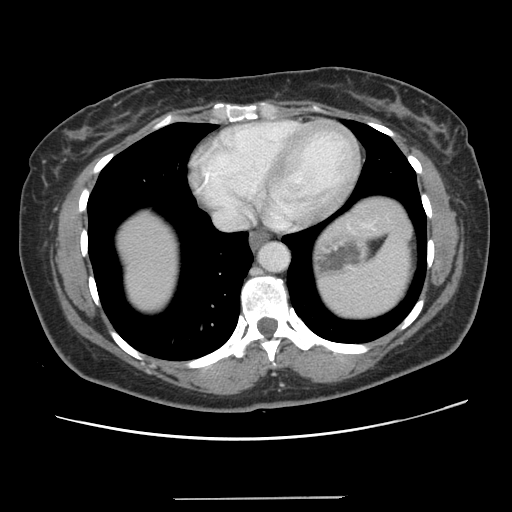
Contrast-enhanced abdominal CT, one axial slice; position 125 of 141 along the scan axis; intravenous contrast given; soft-tissue window (W 400 / L 40 HU); 2.5 mm slice thickness; 512 × 512 image matrix, field of view 366 × 366 mm. Female patient, age 53 years. From the clinical record (not read from this slice): diagnosis: colorectal cancer liver metastases, imaged before liver resection; multiple liver metastases: no; largest metastasis: 14.5 cm; disease in both lobes: yes.
Structures marked on this image (expert manual segmentation):
- liver: bounding box <115,197,405,314> (left, top, right, bottom; pixels)
- planned liver remnant (the part of the liver to remain after resection): <116,217,180,315>